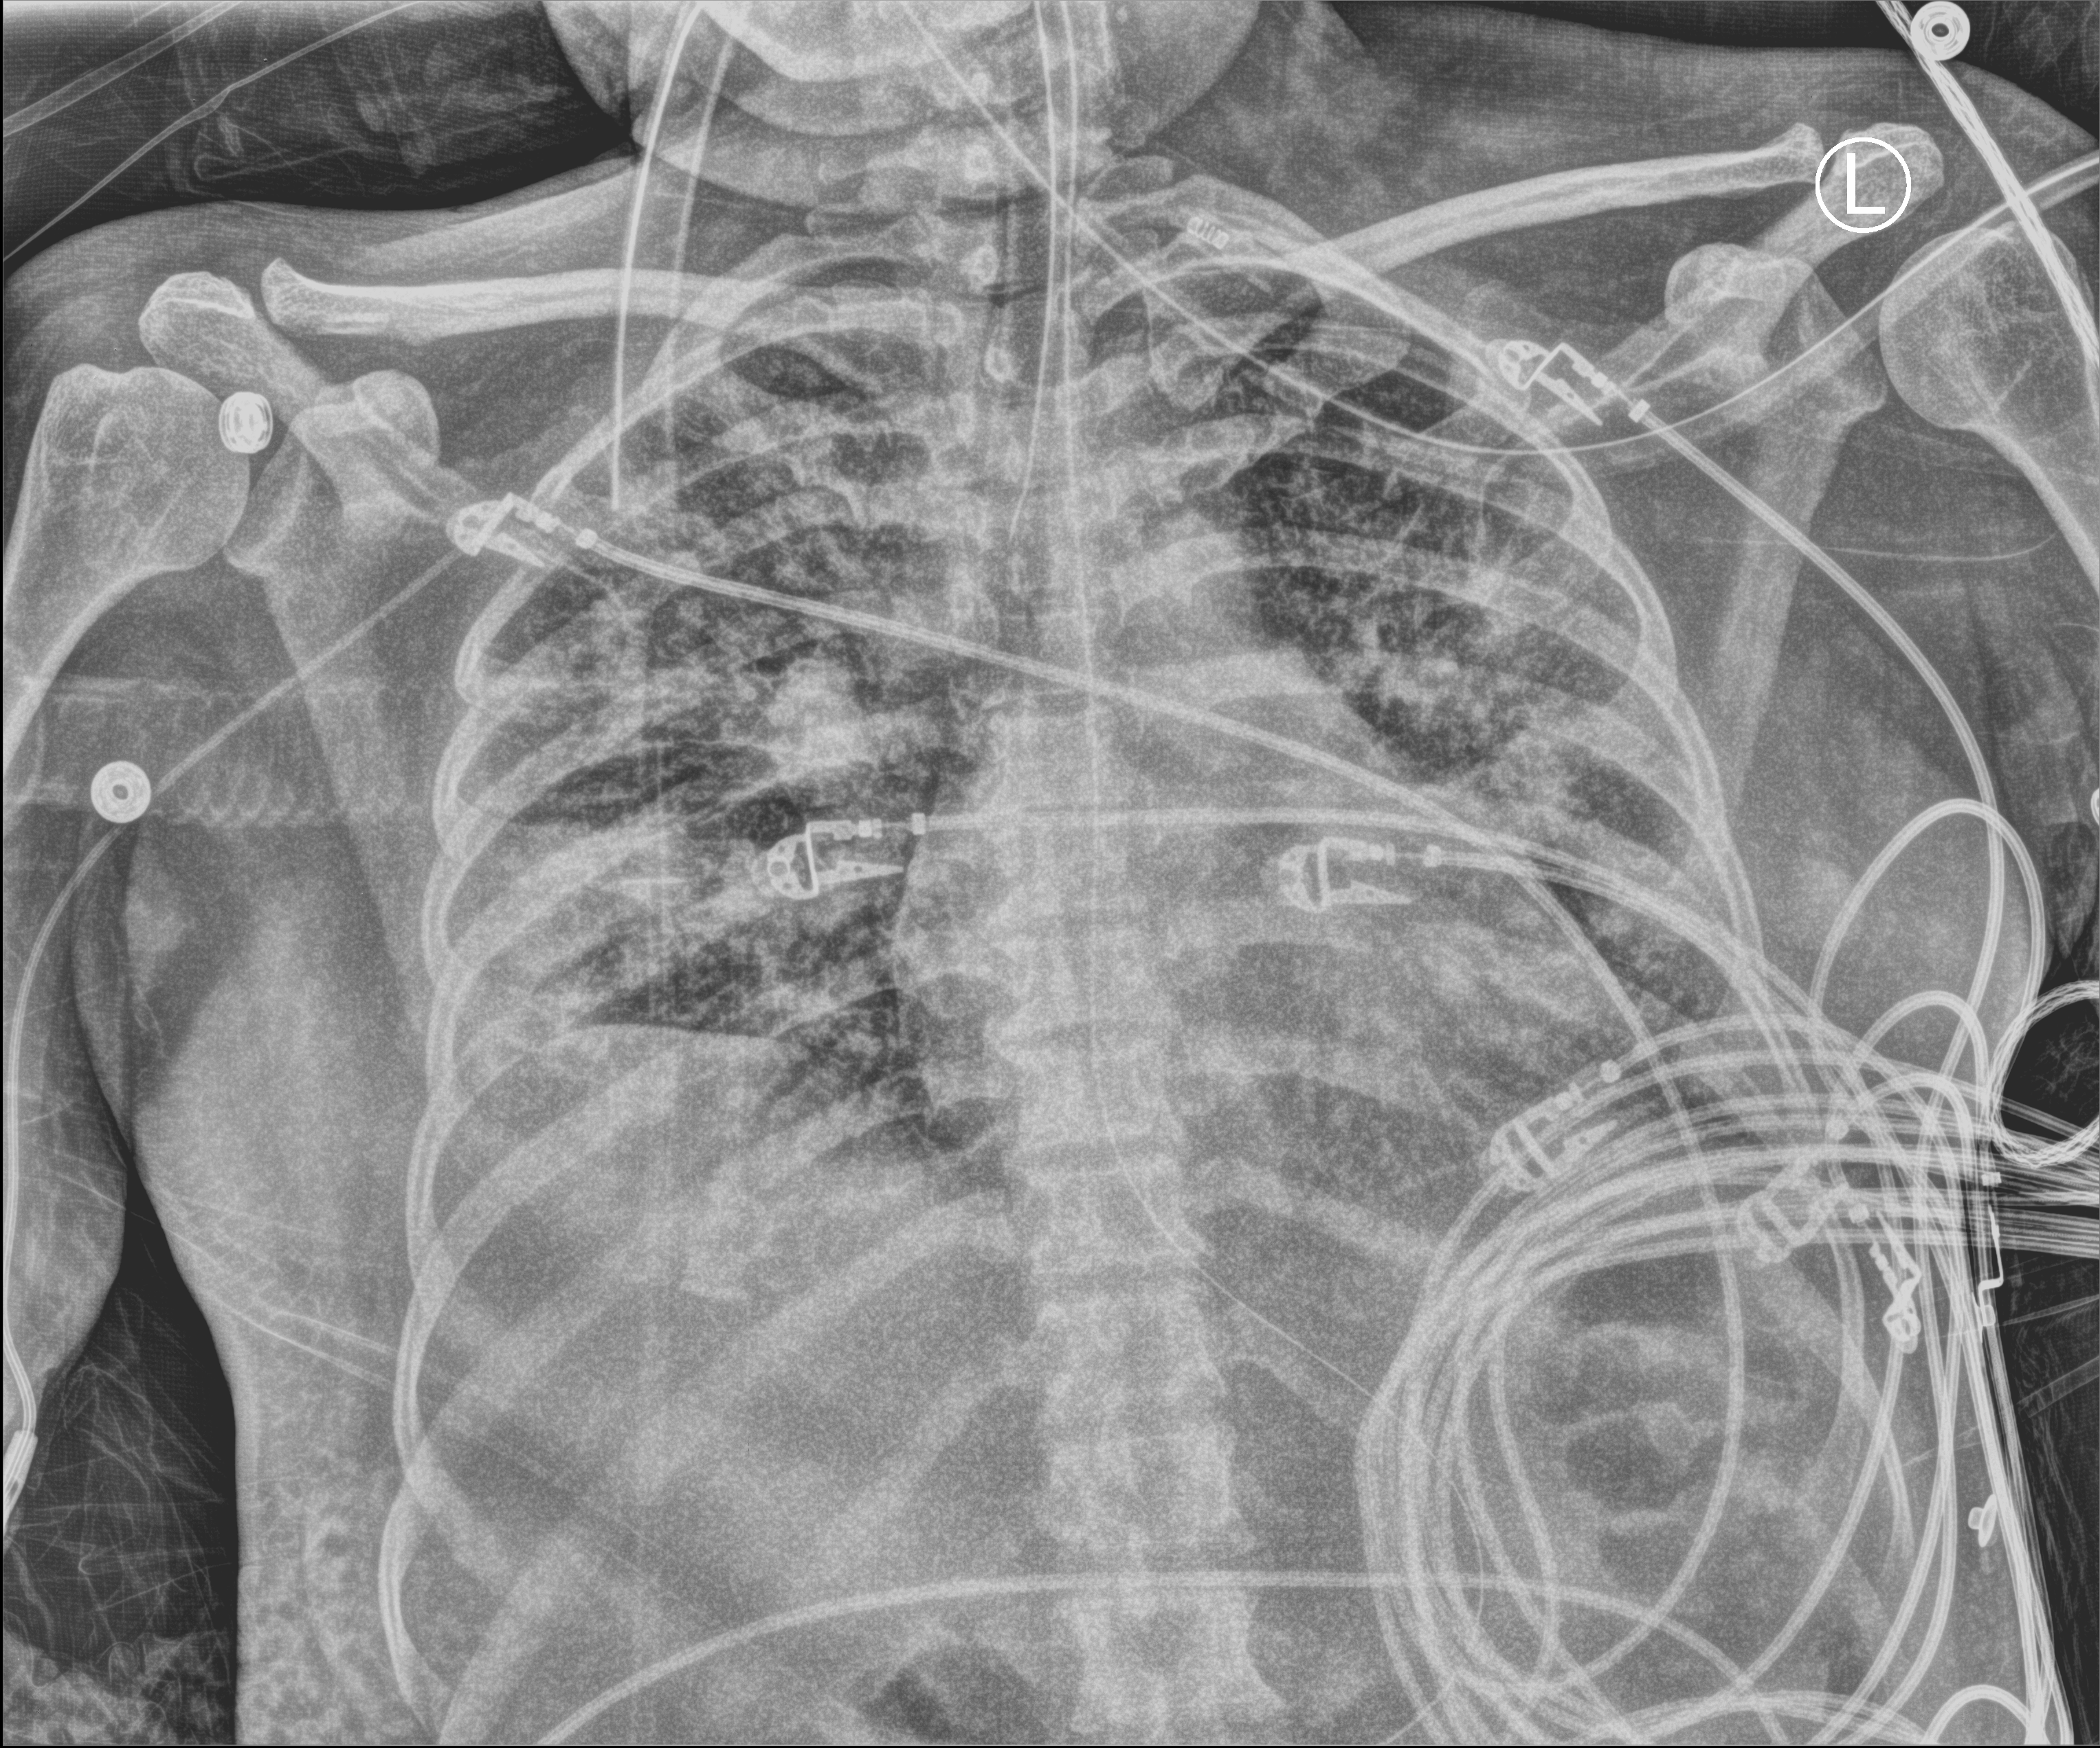
Bedside chest radiograph (computed radiography). Female patient hospitalised with COVID-19, age 18–59 years.
Admission-level facts for this patient (not findings on this image; timing relative to this image not recorded): mechanically ventilated during this hospital stay: yes; COPD (admission record): no; admitted to intensive care during this hospital stay: yes.